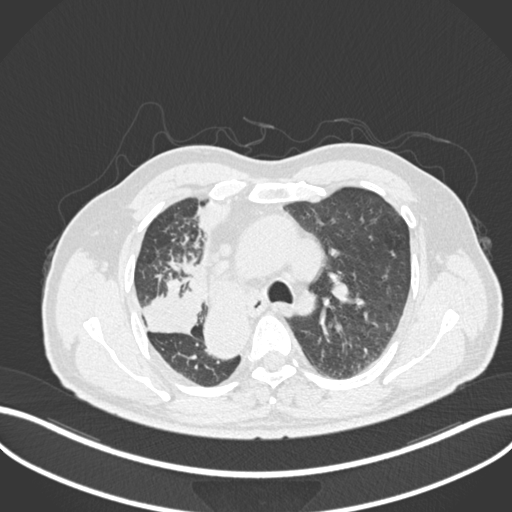
Chest CT, one axial slice; position 164 of 206 along the scan axis; 120 kVp; lung window (W 1500 / L -600 HU); 1 mm slice thickness; 512 × 512 image matrix, field of view 400 × 400 mm. Male patient, age 67 years. Case-level facts recorded for this patient, not image findings: clinical TNM (as recorded): T2a N0 M0.
Structures marked on this image (rectangle marked by the reading radiologist):
- lung tumour (recorded histology: squamous cell carcinoma): bounding box (x1, y1, x2, y2) in pixels: (139, 277, 204, 337)